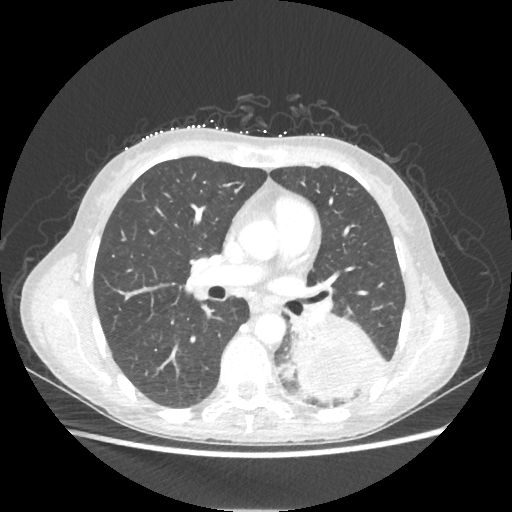
Chest CT, one axial slice; slice 119 of 221 in the series (ordered by position); reconstruction kernel STANDARD; lung window (W 1500 / L -600 HU); 1.25 mm slice thickness; 512 × 512 image matrix. Female patient, age 53 years. From the clinical record (not read from this slice): clinical TNM (as recorded): T3 N0 M0.
Structures marked on this image (rectangle marked by the reading radiologist):
- lung tumour (recorded histology: adenocarcinoma): bounding box <291,318,387,403> (left, top, right, bottom; pixels)